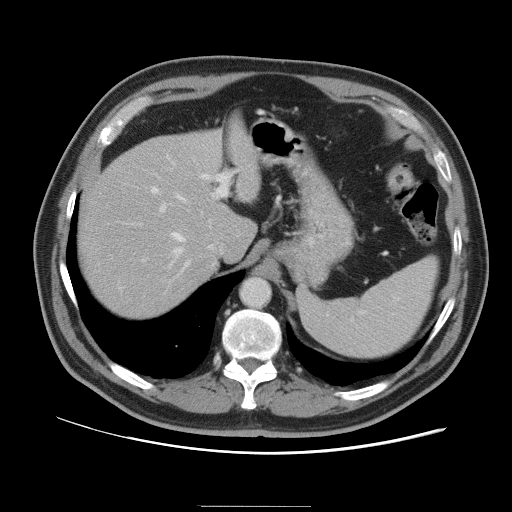
Contrast-enhanced abdominal CT, one axial slice. Position 74 of 105 along the scan axis. Intravenous contrast given. Soft-tissue window (W 400 / L 40 HU). 512 × 512 image matrix, field of view 399 × 399 mm. Male patient, age 64 years. From the clinical record (not read from this slice): diagnosis: colorectal cancer liver metastases, imaged before liver resection; multiple liver metastases: yes; largest metastasis: 3 cm; disease in both lobes: yes.
Outlined on this slice (manually delineated by an expert):
- hepatic veins: bounding box [x1, y1, x2, y2] px = [171, 194, 187, 256]
- liver: [78, 122, 259, 318]
- planned liver remnant (the part of the liver to remain after resection): [78, 145, 253, 318]
- portal vein (with intrahepatic branches): [151, 161, 229, 272]